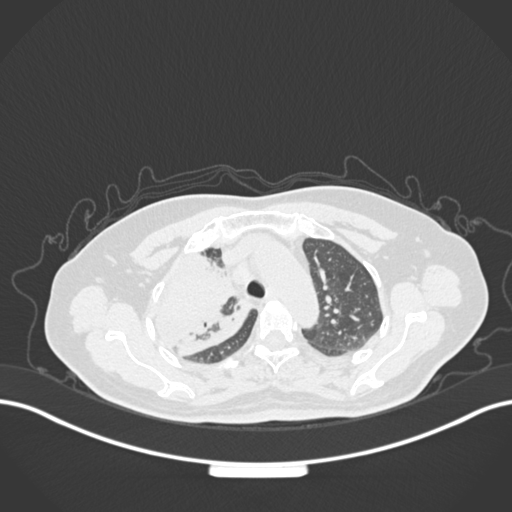
Chest CT, one axial slice. Slice 120 of 177 in the series (ordered by position). 120 kVp. Lung window (W 1500 / L -600 HU). 1 mm slice thickness. 512 × 512 image matrix. Female patient, age 60 years. From the clinical record (not read from this slice): clinical TNM (as recorded): T3 N1 M1.
Annotated regions visible in this slice (bounding box drawn by a radiologist):
- lung tumour (recorded histology: adenocarcinoma): box from (x=146, y=239) to (x=238, y=351) px